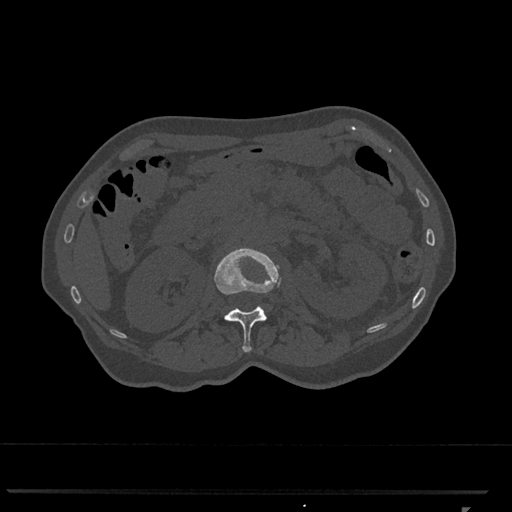
CT including the spine, one axial slice. Position 388 of 793 along the scan axis. Reconstruction kernel Br40s/3. 120 kVp. Bone window (W 1800 / L 400 HU). 0.5 mm slice thickness. 512 × 512 image matrix, field of view 380 × 380 mm. Patient: female, 62 years. Case-level facts recorded for this patient, not image findings: primary cancer: renal.
Annotated regions visible in this slice (semi-automatically segmented with operator editing):
- L1 vertebra: bounding box (x1, y1, x2, y2) in pixels: (214, 248, 281, 352)